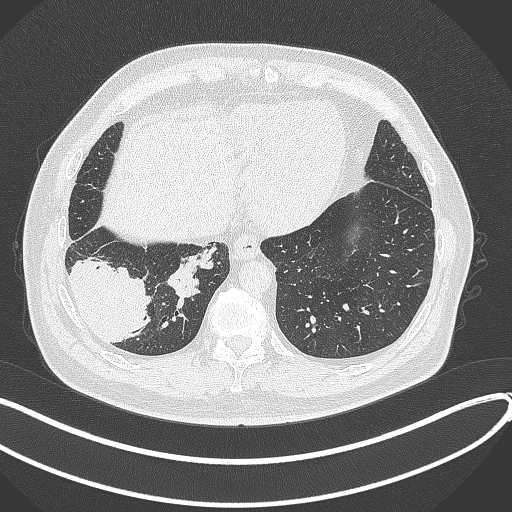
Chest CT, one axial slice. Slice 82 of 360 in the series (ordered by position). Reconstruction kernel B70f. Lung window (W 1500 / L -600 HU). 1 mm slice thickness. 512 × 512 image matrix, field of view 400 × 400 mm. Patient: male, 59 years.
Annotated regions visible in this slice (rectangle marked by the reading radiologist):
- lung tumour (recorded histology: adenocarcinoma): bounding box (x1, y1, x2, y2) in pixels: (64, 257, 156, 346)